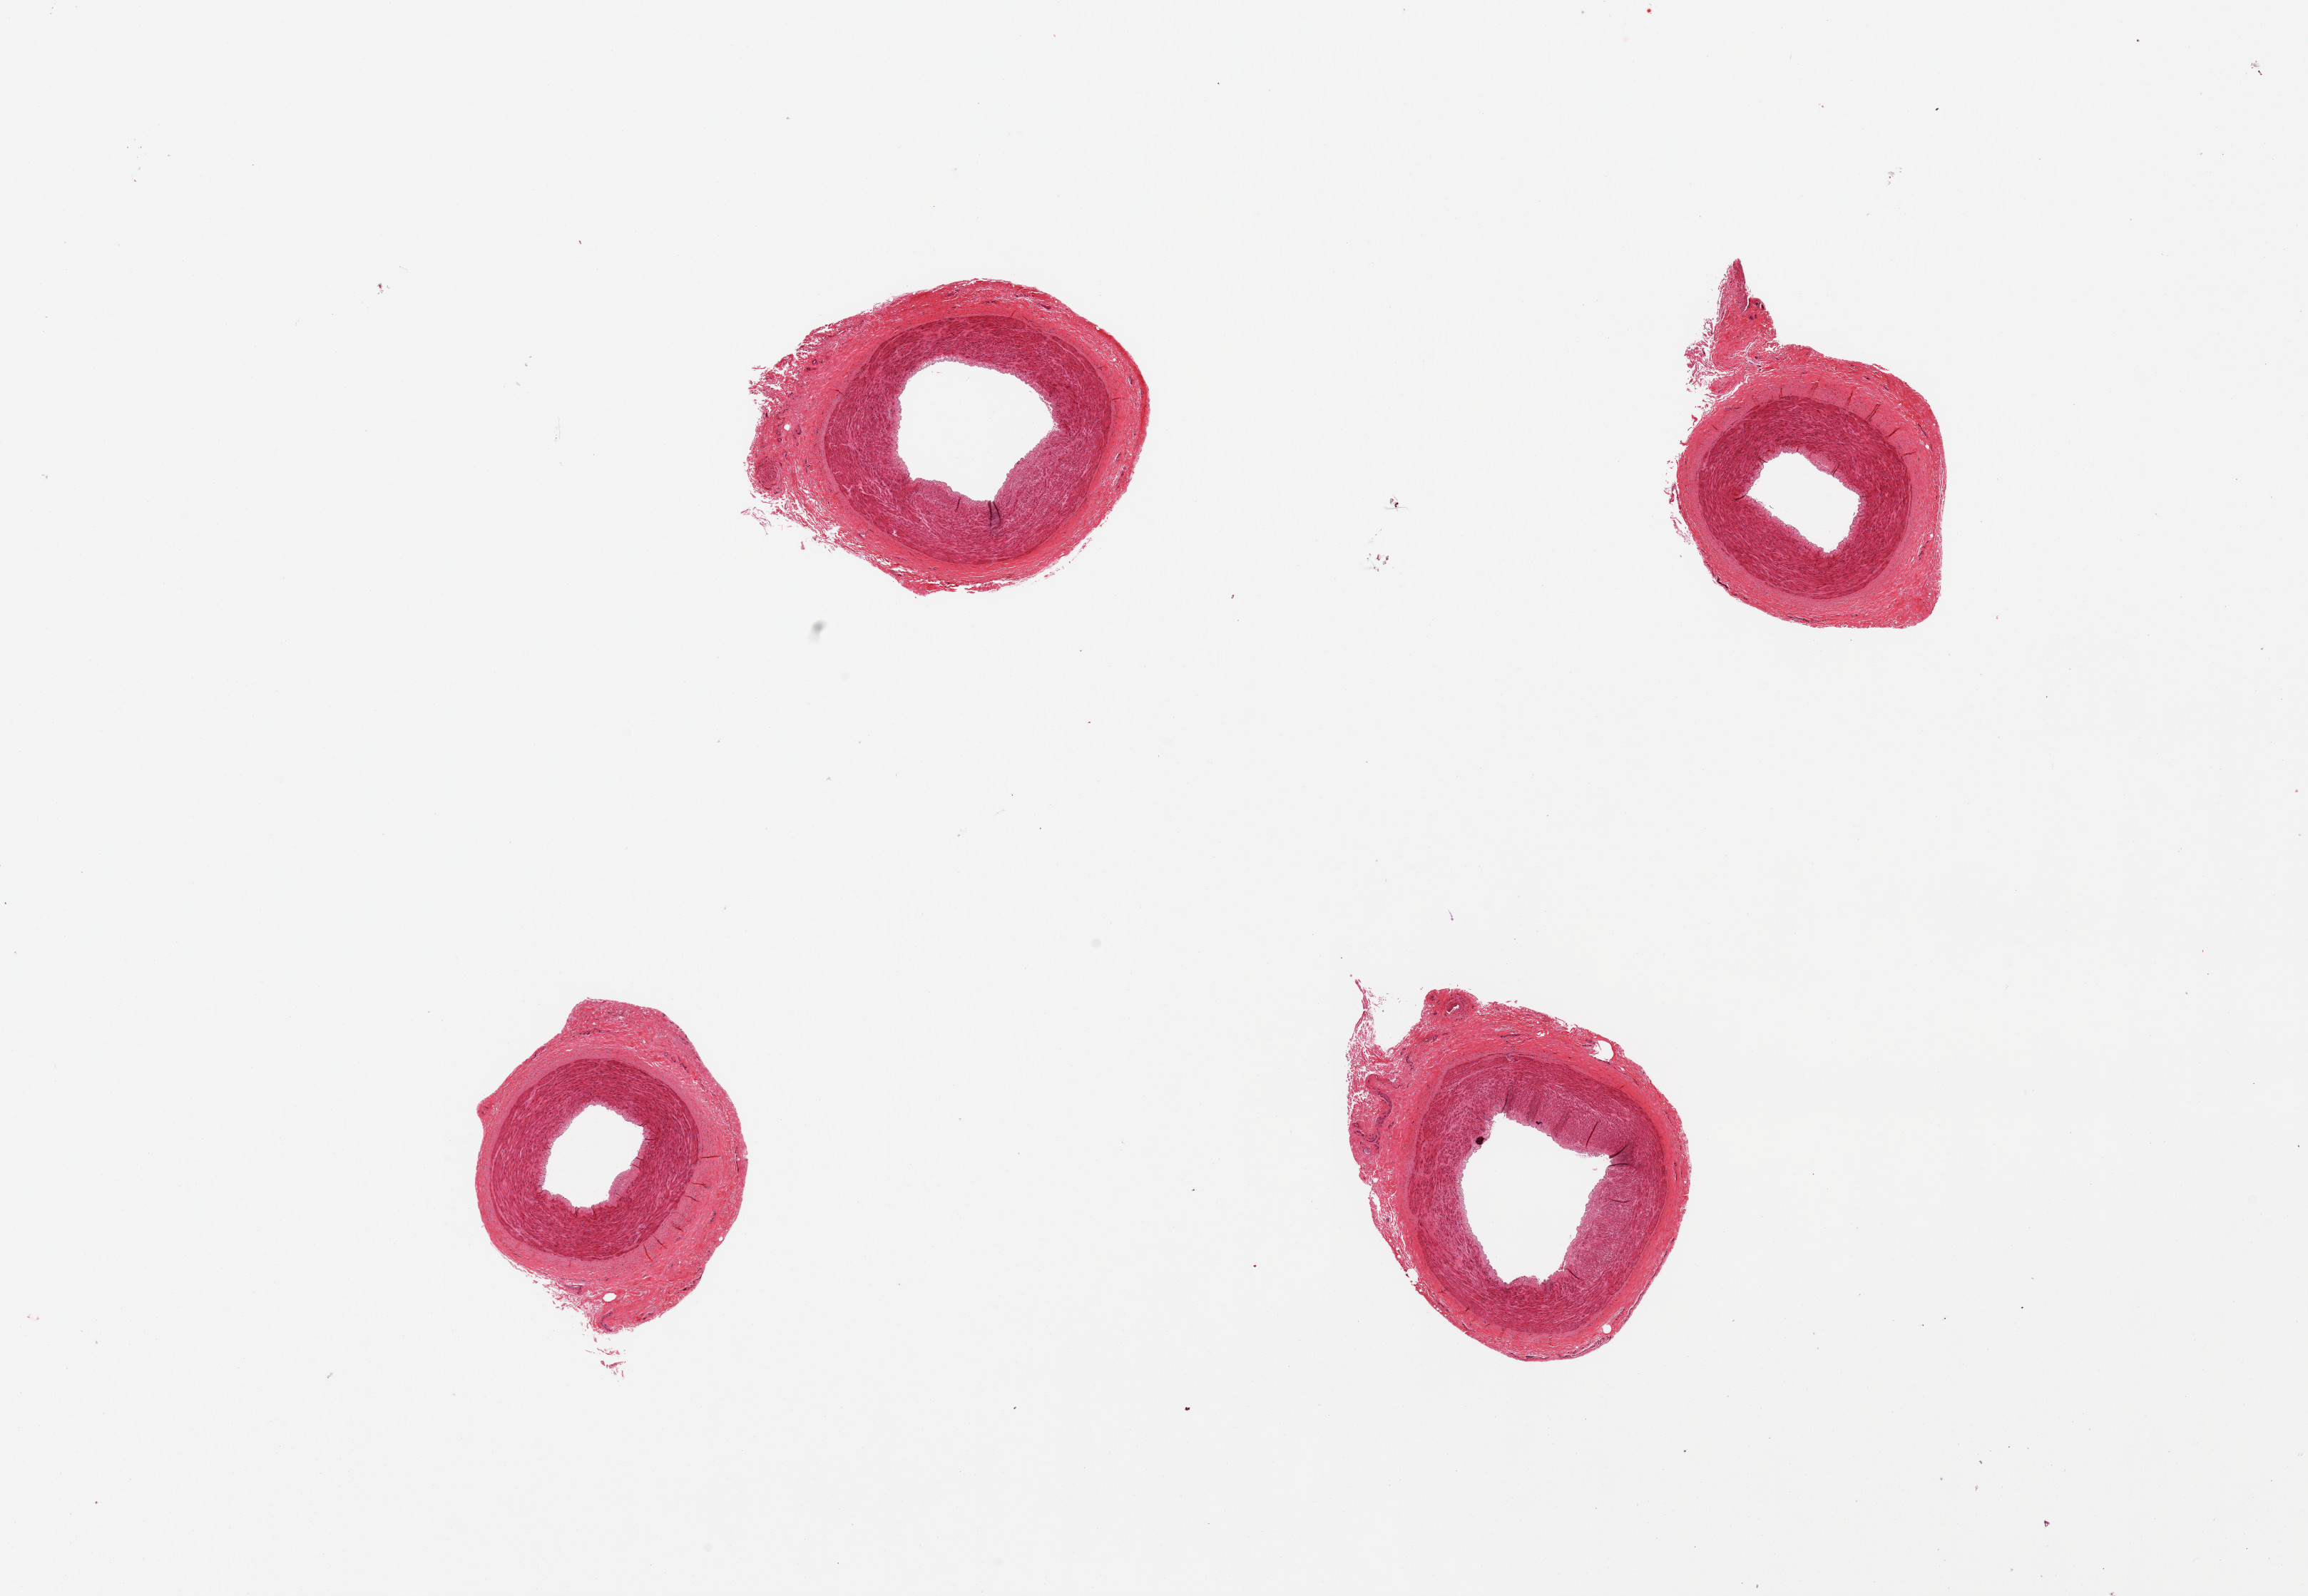
Digitized H&E-stained section, brightfield, whole scanned area (about 25.6 x 17.7 mm, from a 20x scan) shown as a low-resolution overview. PAXgene-fixed paraffin-embedded (PFPE) section. Section of tibial artery (target tissue). Tissue donor sample.
Review note (as recorded): 4 pieces, good clean specimens.